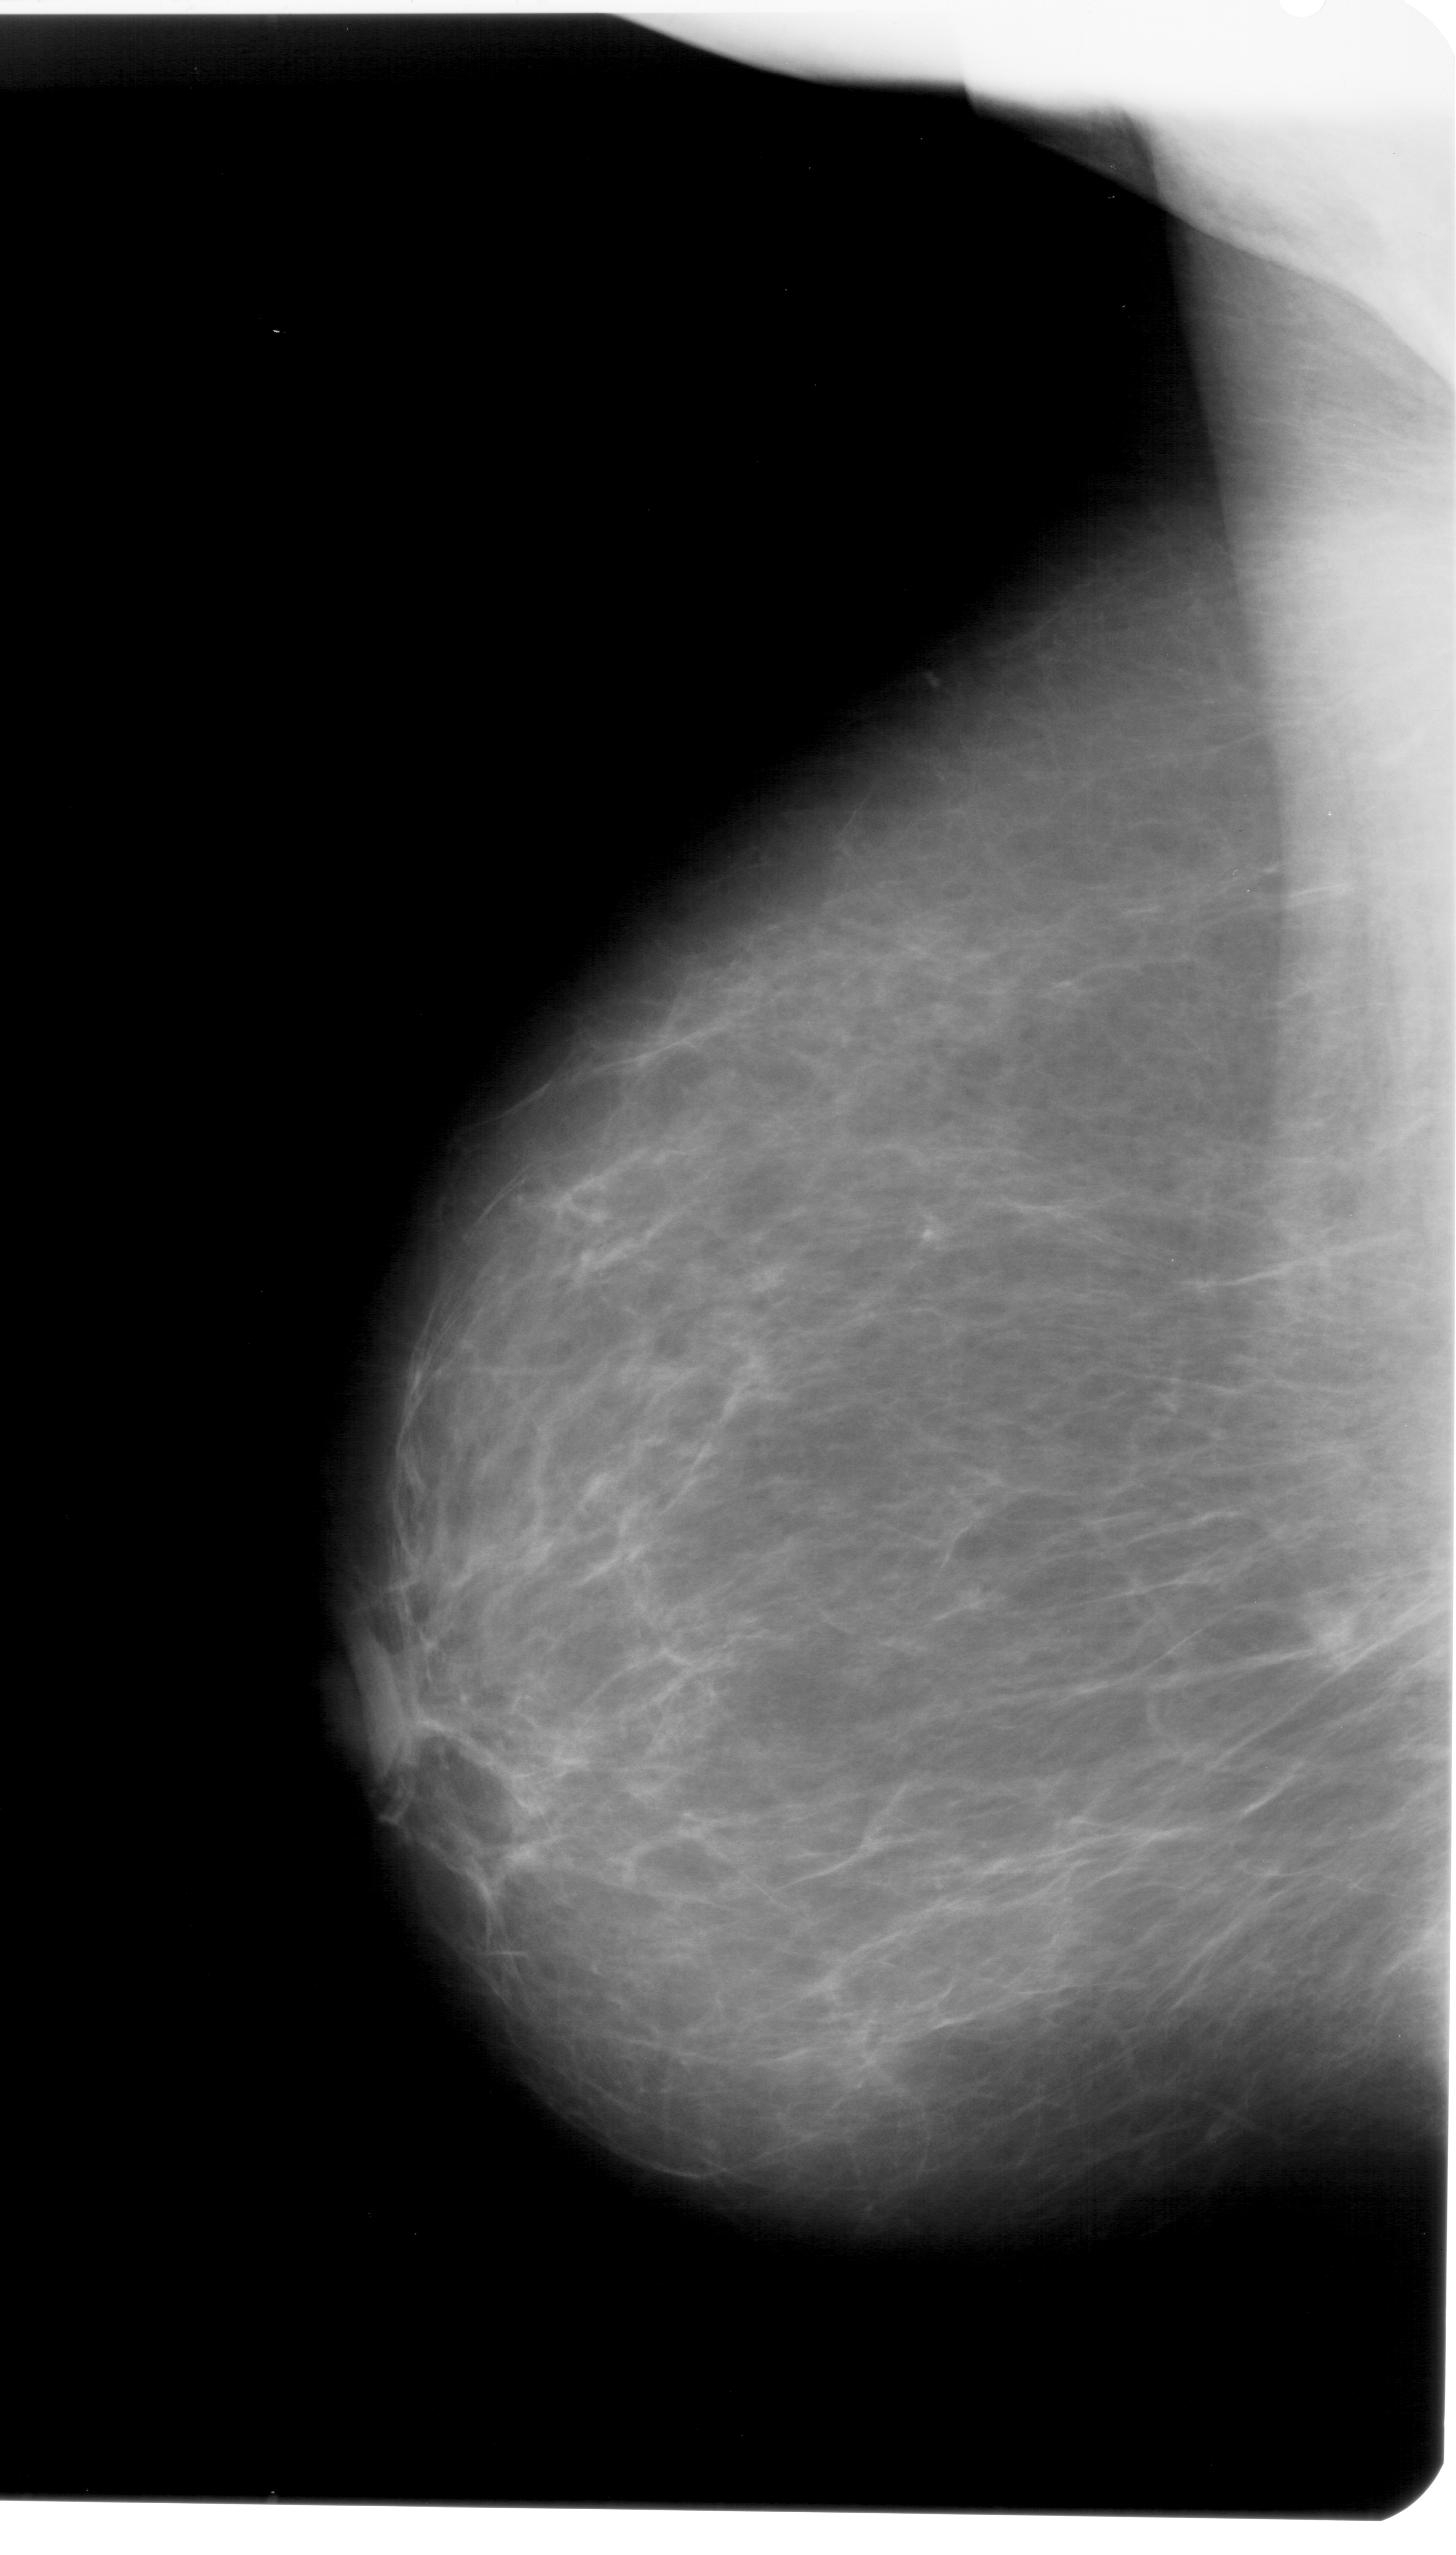
Scanned film-screen mammogram. Left breast. MLO view. BI-RADS breast density category 2 (scale 1–4). 1456 × 2555 image matrix.
Expert-marked regions of interest on this film, with their recorded descriptors:
- mass, shape oval, margins ill defined; BI-RADS assessment category 5; pathology (as recorded): malignant: bounding box <1292,1587,1380,1671> (left, top, right, bottom; pixels)